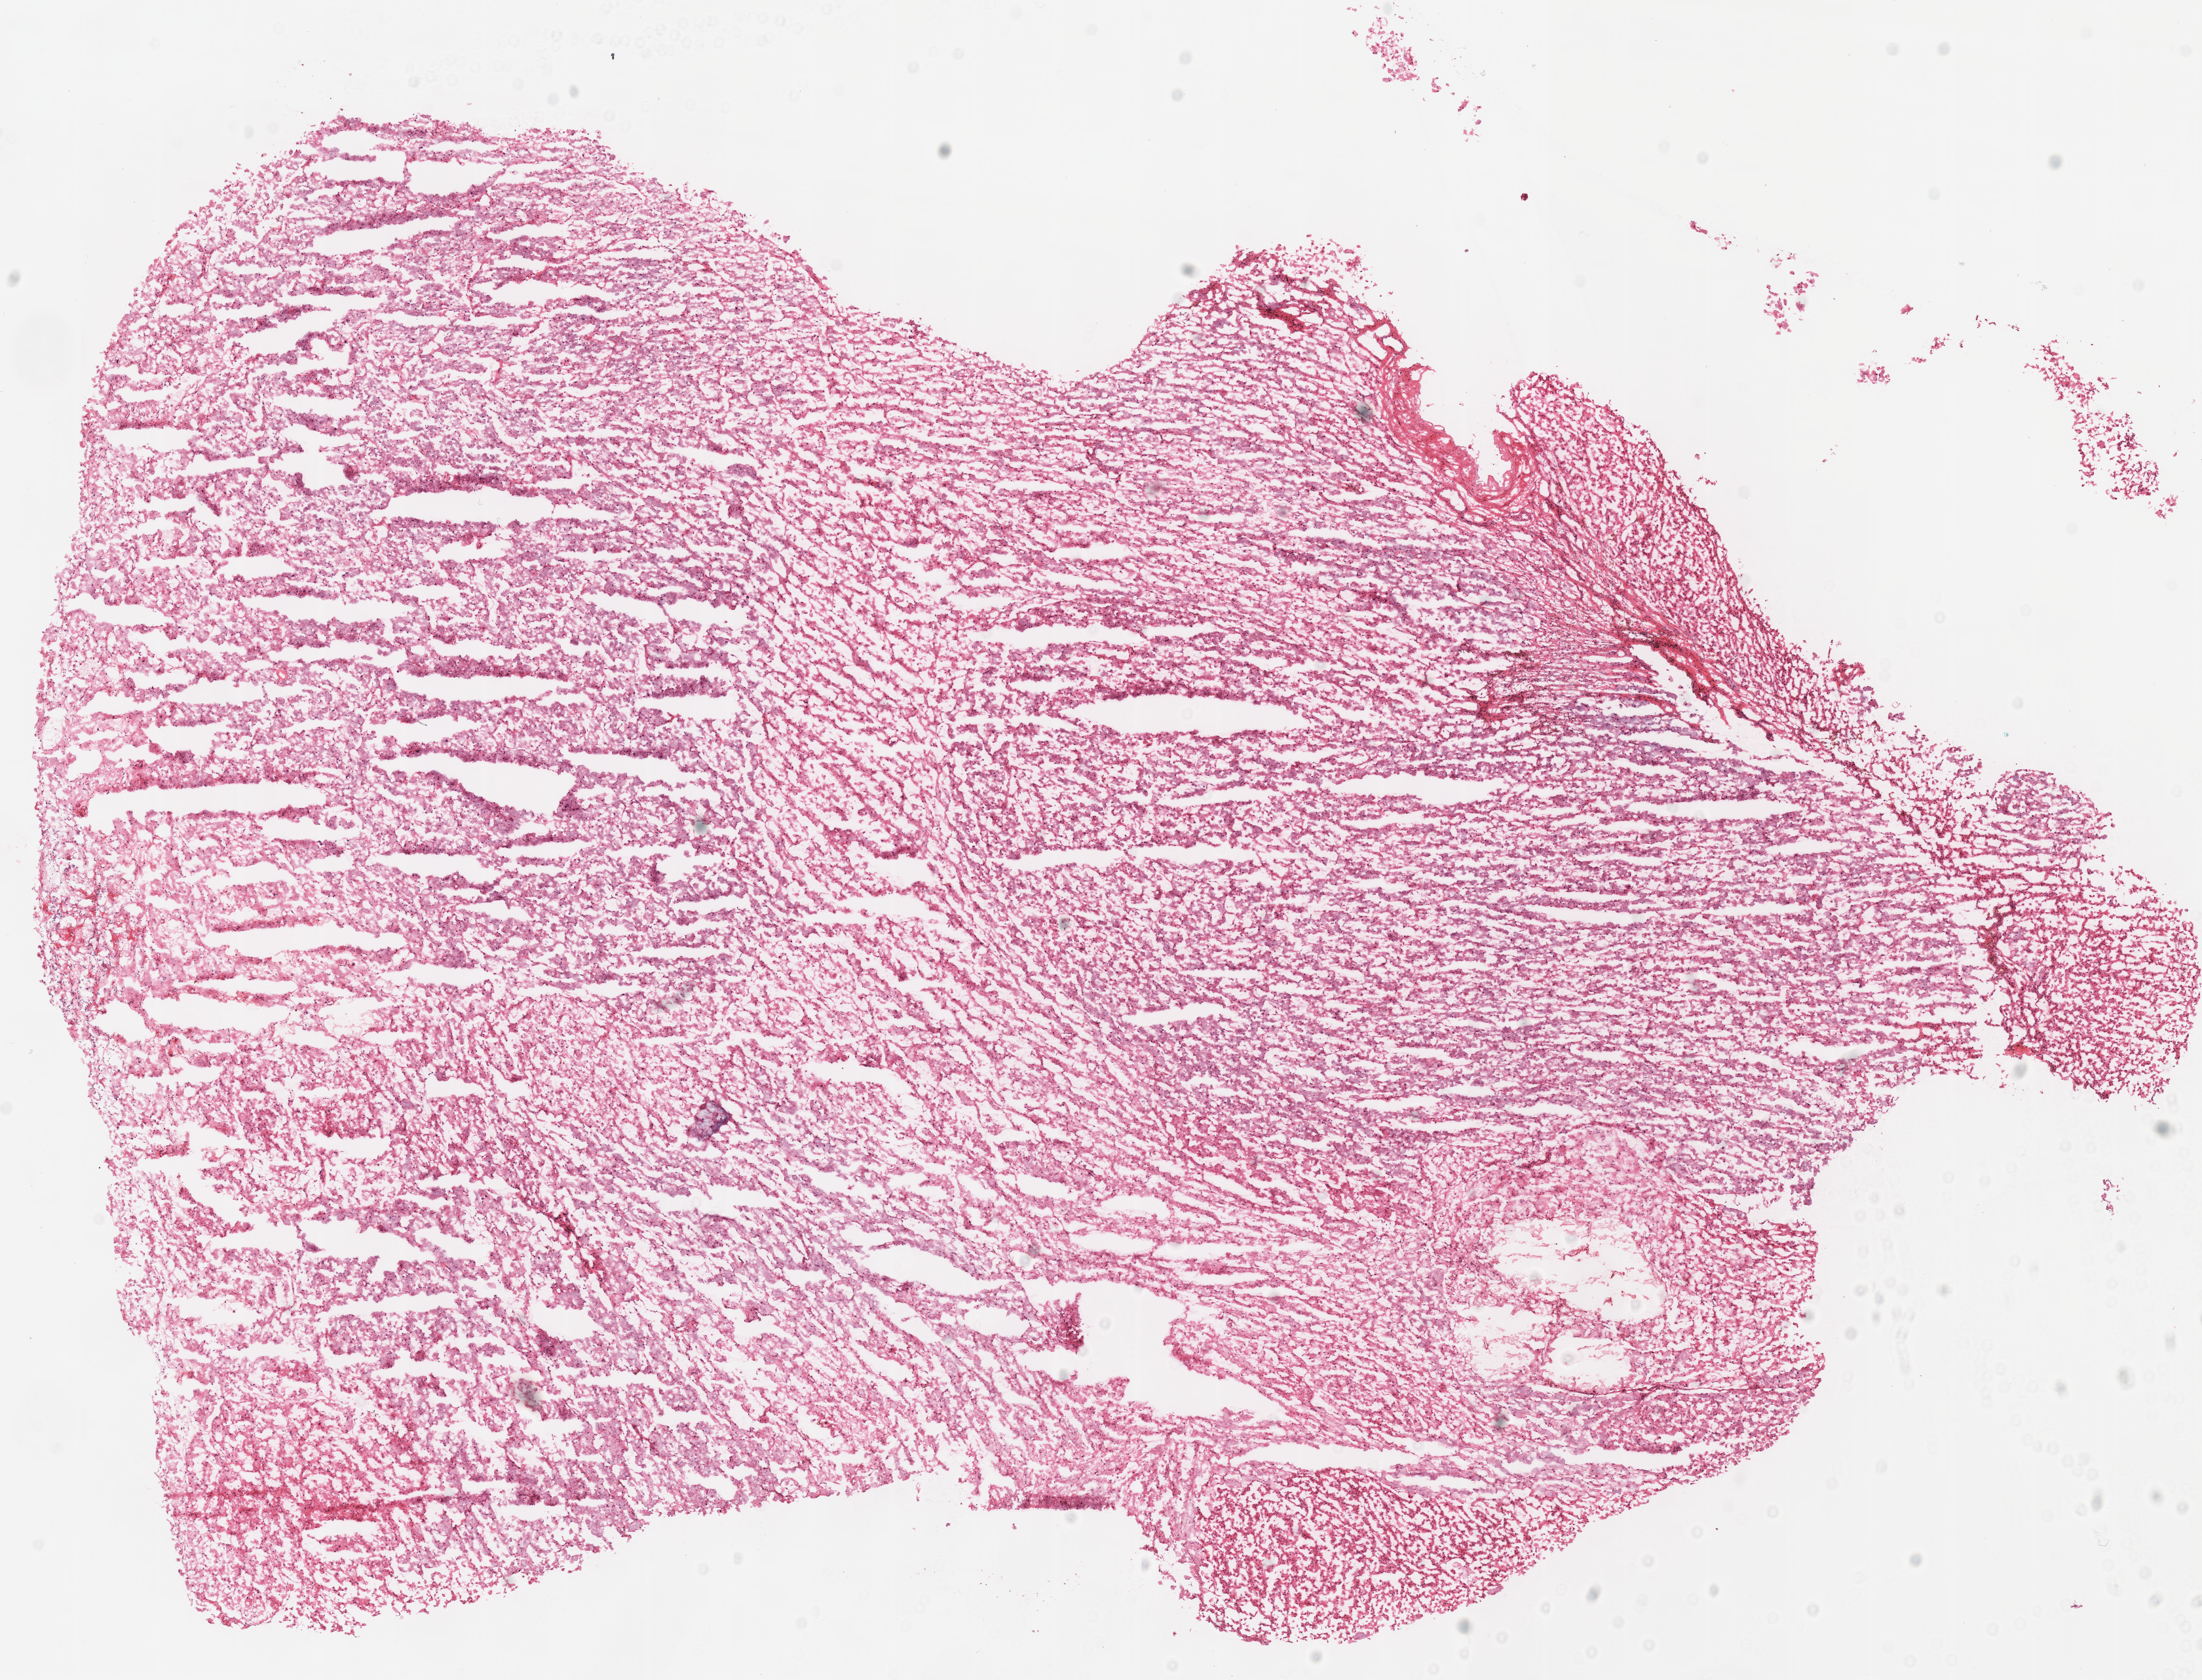
Whole-slide histology image, H&E-stained, a low-resolution overview of the entire scanned area, about 13.2 x 10.1 mm (acquisition: 40x scan), frozen section, sample: primary tumour, kidney. Female patient; age at initial diagnosis 46 years. Slide review estimates, as recorded: tumour cells 100%, tumour nuclei 95%, normal cells 0%, stromal cells 0%, necrosis 0%. Infiltration values recorded for this section: lymphocyte infiltration 0%, monocyte infiltration 0%, neutrophil infiltration 0%.
AJCC pathologic stage: III (6th edition). Diagnosis: Renal cell carcinoma, chromophobe type.